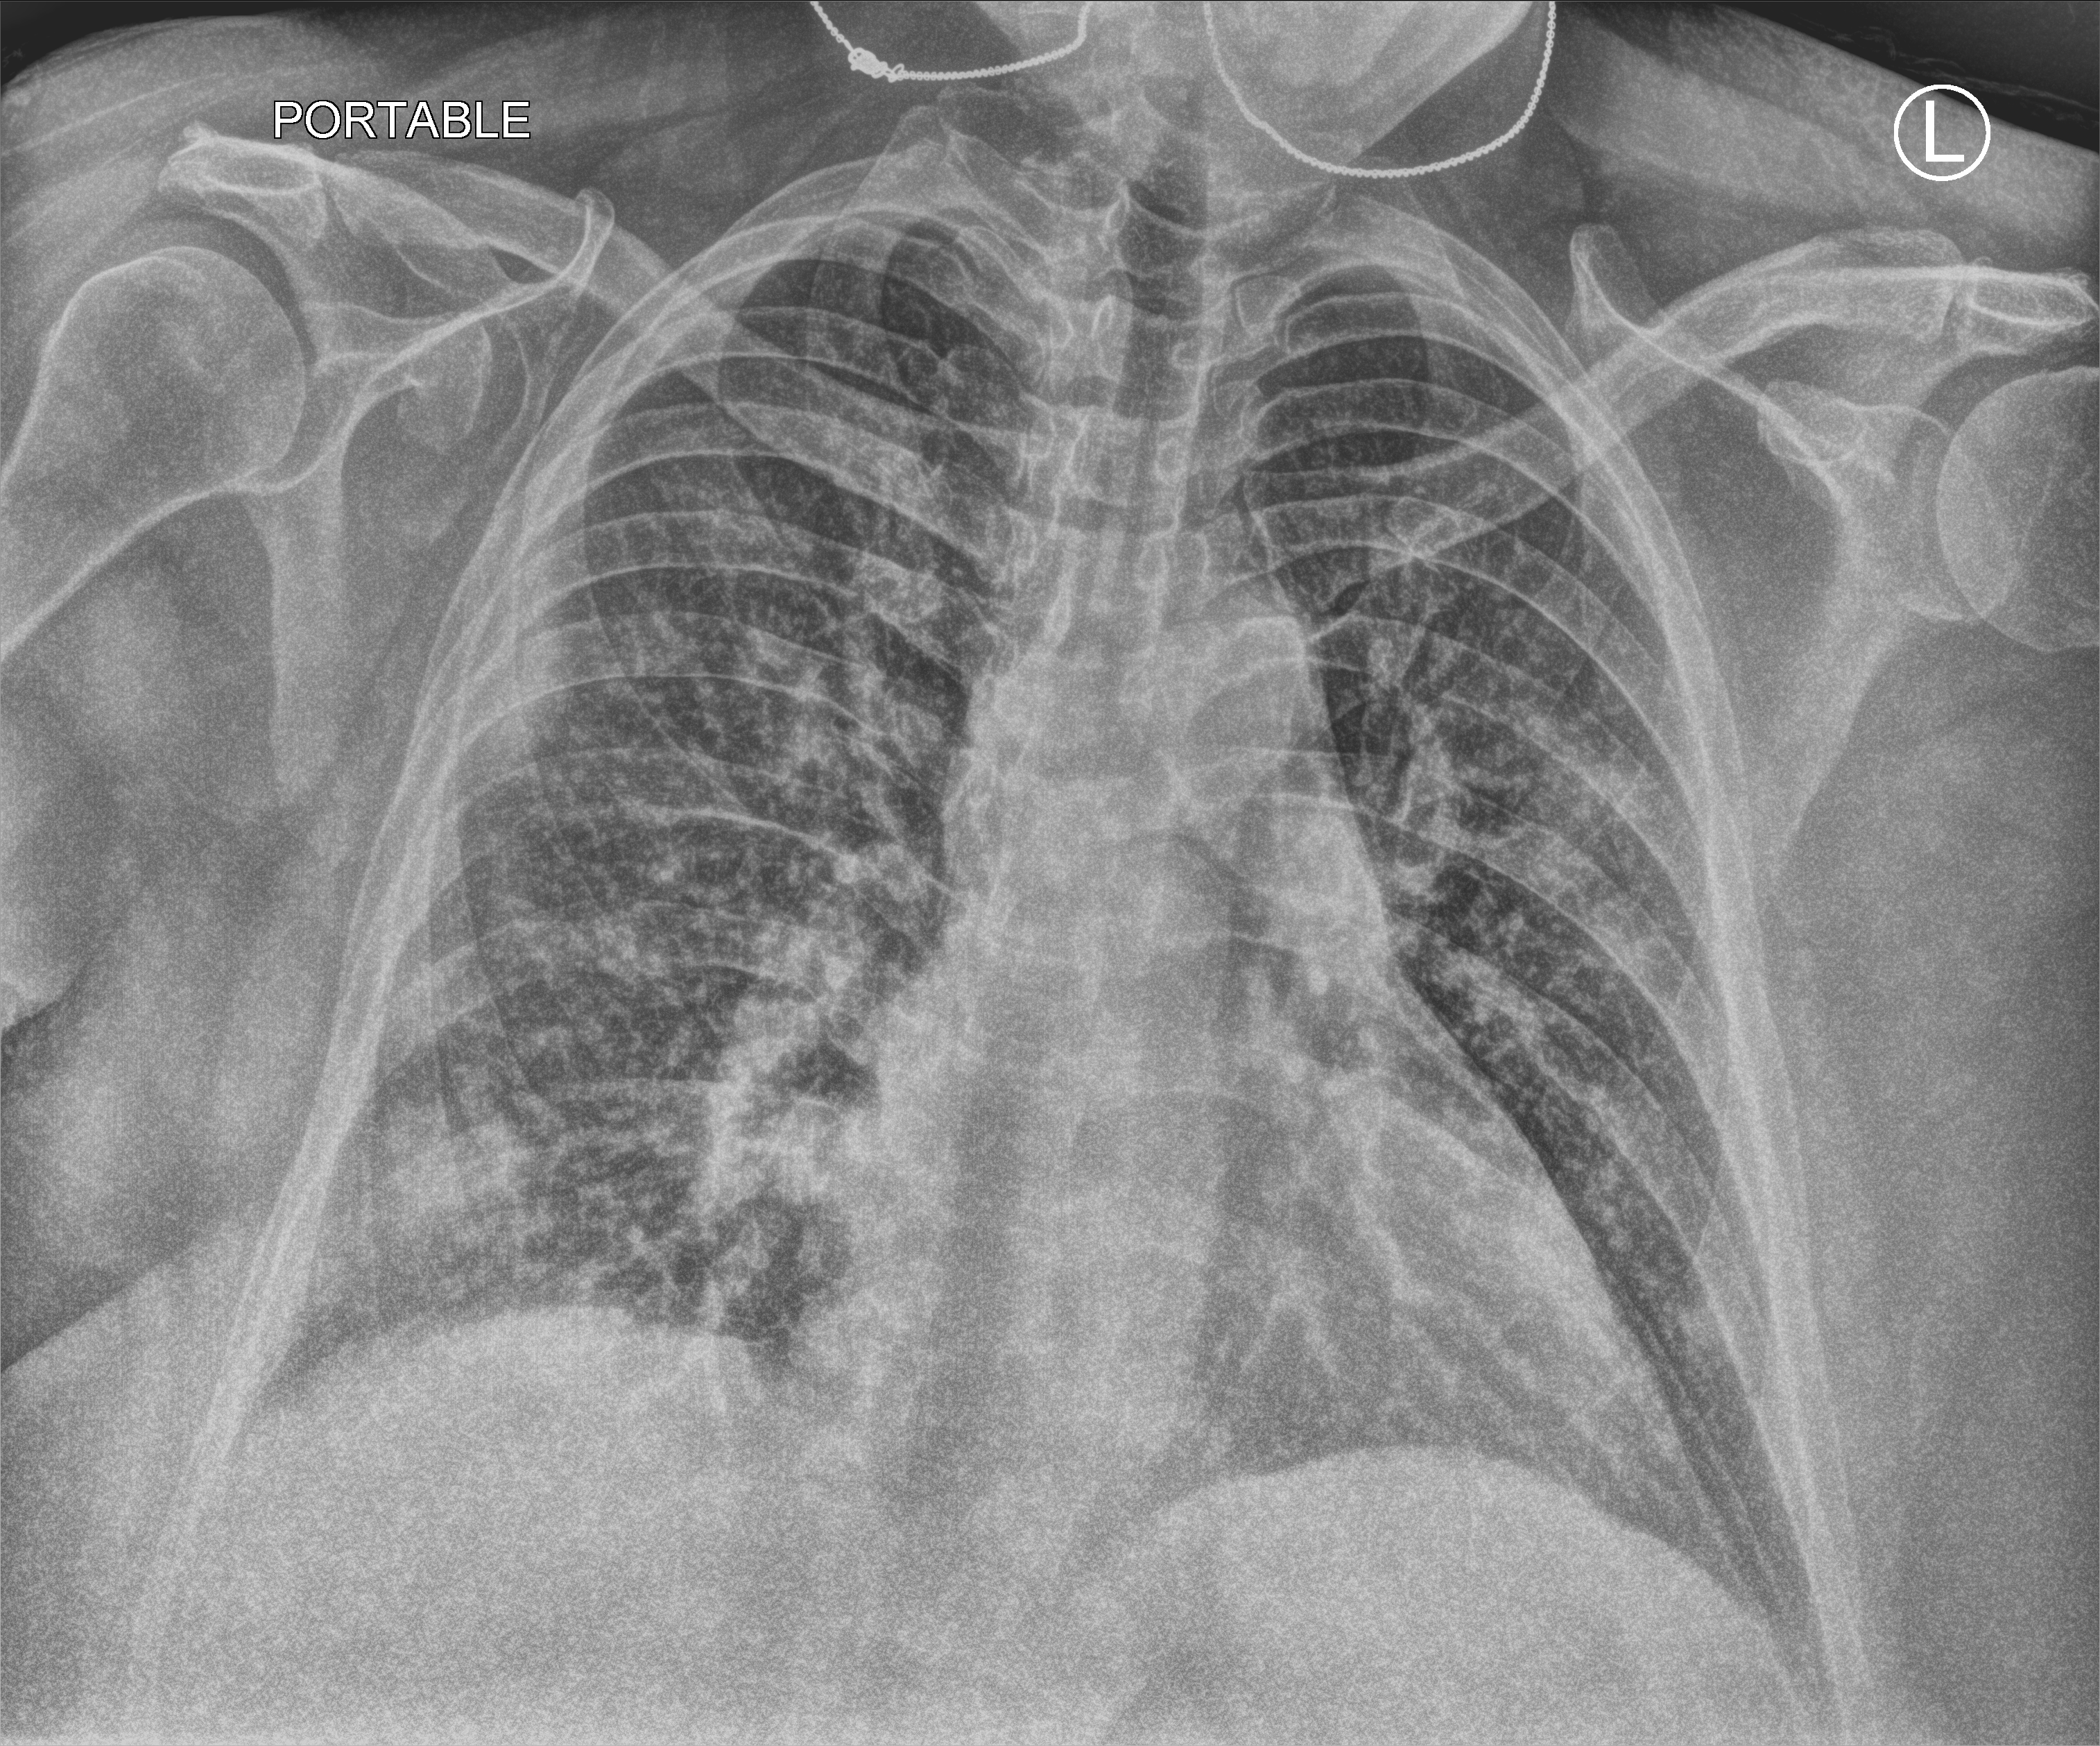
Bedside chest radiograph (computed radiography); anteroposterior (AP) projection. Female patient hospitalised with COVID-19, age 60–74 years.
From the hospital-stay record, not from the radiograph (when in the stay this image was taken is not recorded):
- admitted to intensive care during this hospital stay: no
- mechanically ventilated during this hospital stay: no
- other chronic lung disease (admission record): no